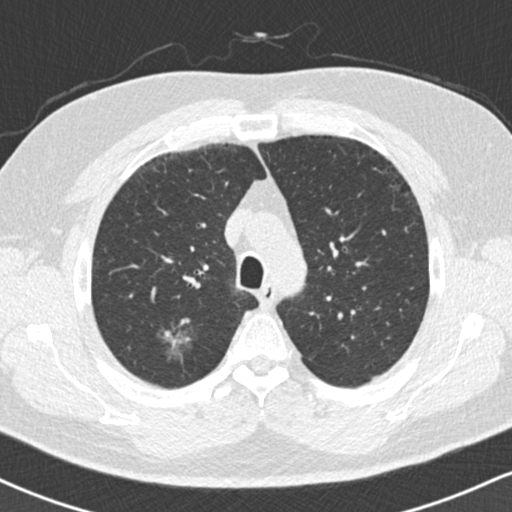
Low-dose screening chest CT, one axial slice. Position 126 of 169 along the scan axis. Reconstruction kernel B30f. 120 kVp. Lung window (W 1500 / L -600 HU). 2 mm slice thickness. 512 × 512 image matrix, field of view 320 × 320 mm.
Structures marked on this image (manually delineated by an expert):
- lesion 1 (tumor, upper lobe of right lung): box from (x=163, y=330) to (x=189, y=359) px